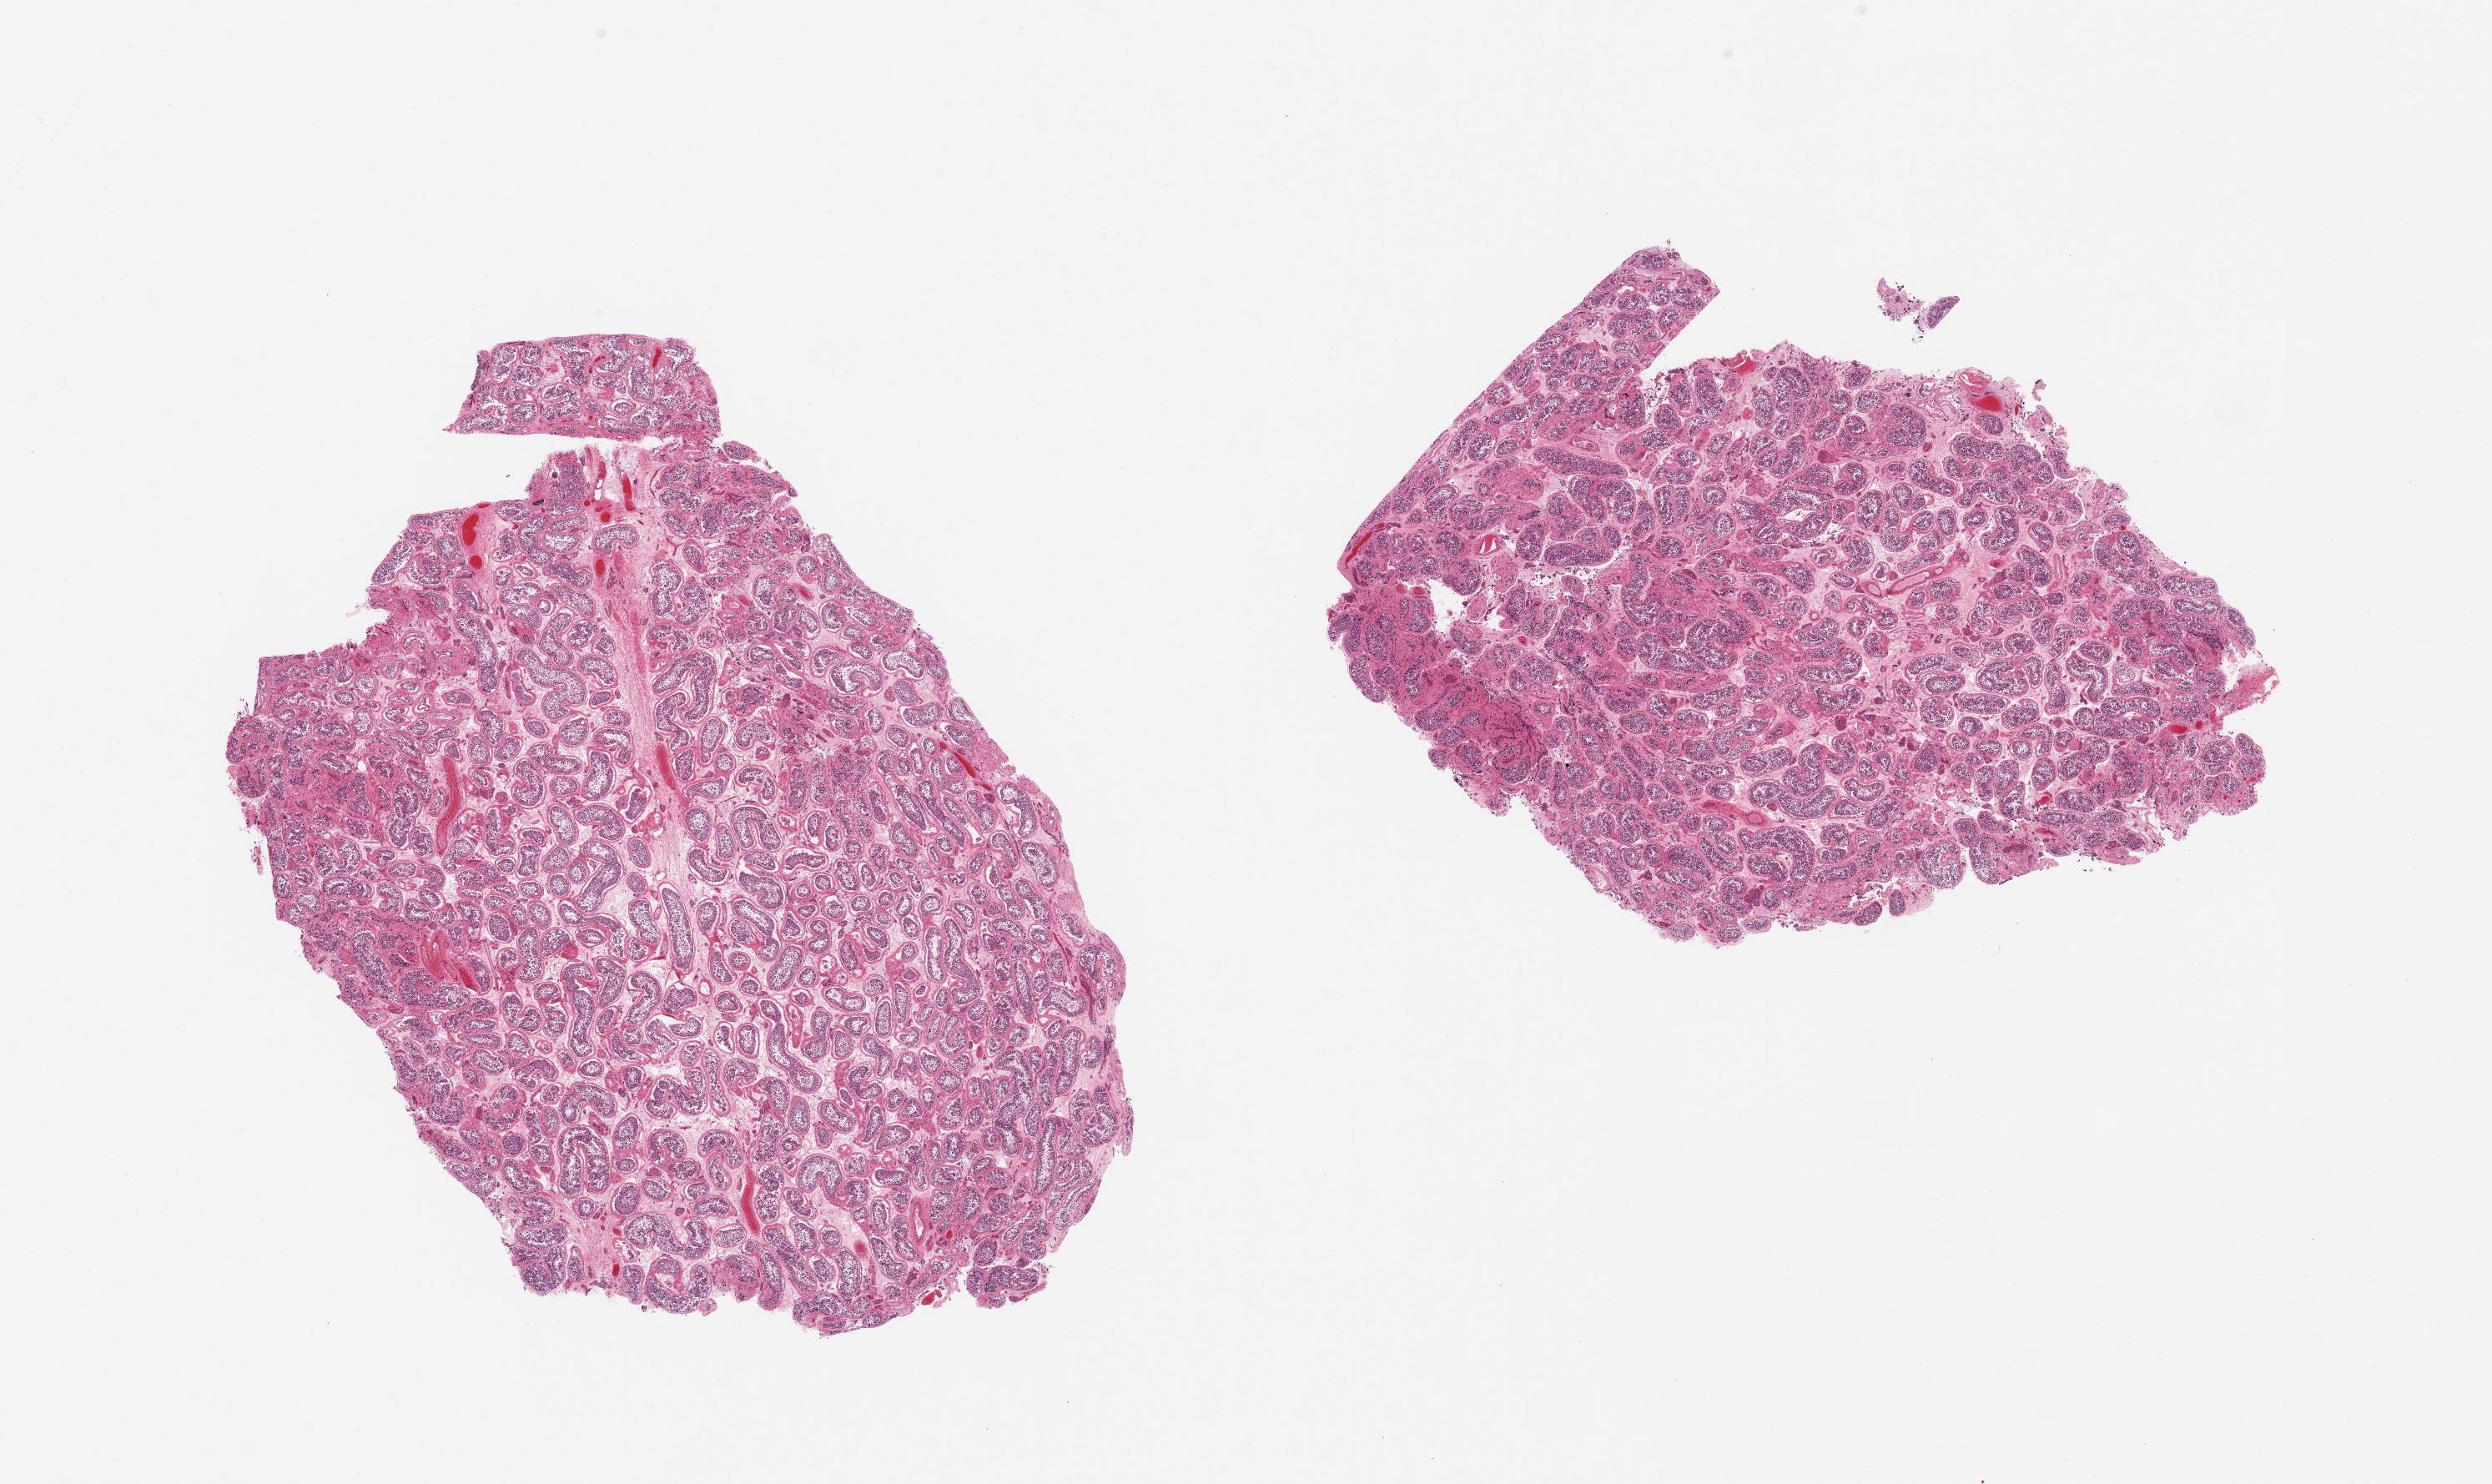
H&E whole-slide image — a low-resolution overview of the entire scanned area, about 23.6 x 14.1 mm. PAXgene-fixed paraffin-embedded (PFPE) section. Section of testis (target tissue). Tissue donor sample.
Pathologist's review note for this sample: 2 pieces, moderate atrophy. Reduced spermatogenesis, marked.